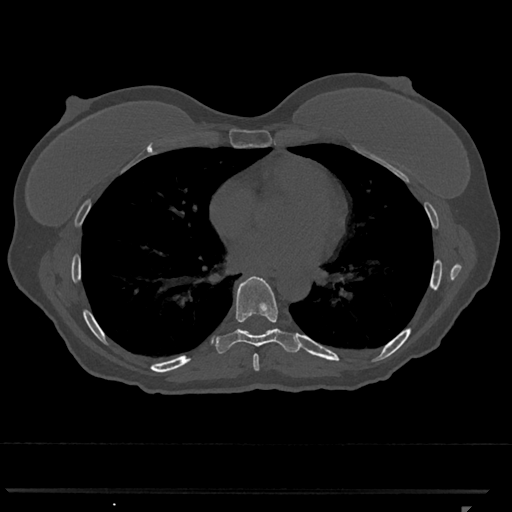
CT including the spine, one axial slice. Slice 668 of 793 in the series (ordered by position). 120 kVp. Bone window (W 1800 / L 400 HU). 0.5 mm slice thickness. 512 × 512 image matrix. Female patient, age 62 years. Case-level facts recorded for this patient, not image findings: primary cancer: renal.
Outlined on this slice (semi-automatically segmented with operator editing):
- T7 vertebra: box from (x=253, y=354) to (x=259, y=371) px
- T8 vertebra: (x=216, y=276)–(x=299, y=354)